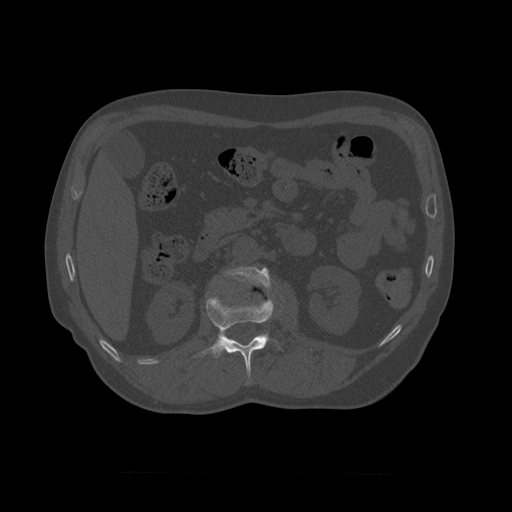
CT including the spine, one axial slice. Slice 350 of 450 in the series (ordered by position). Reconstruction kernel STANDARD. 120 kVp. Bone window (W 1800 / L 400 HU). 1.25 mm slice thickness. 512 × 512 image matrix, field of view 405 × 405 mm. Patient age 75 years. From the clinical record (not read from this slice): primary cancer: prostate.
Annotated regions visible in this slice (semi-automatic segmentation, software-assisted and operator-edited):
- L1 vertebra: bounding box [x1, y1, x2, y2] px = [194, 291, 277, 385]
- L2 vertebra: [220, 266, 272, 295]